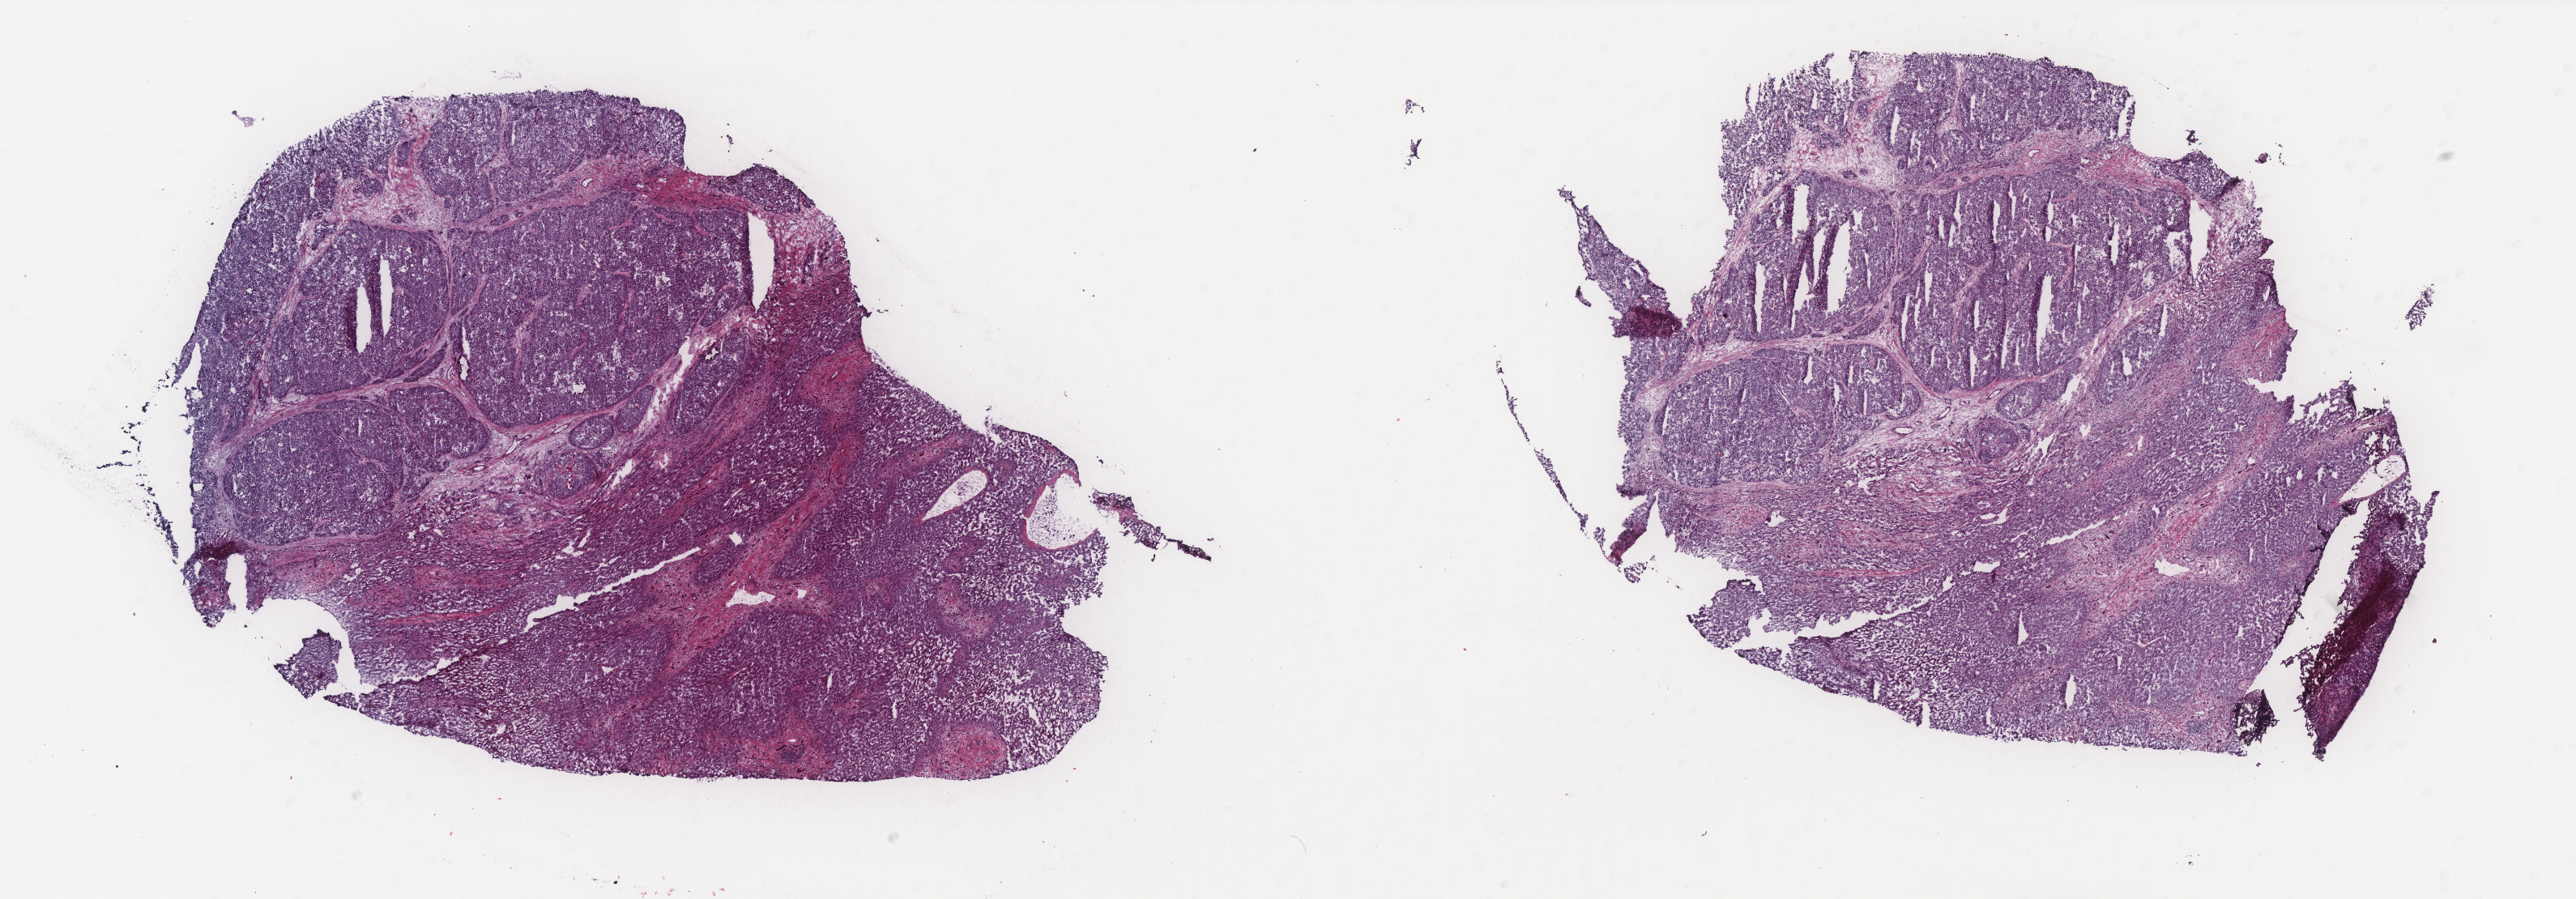
Digitized H&E tissue section (whole slide) — shown as a low-resolution overview of the whole scanned area (about 25.5 x 8.9 mm, slide scanned at 40x); frozen section; liver, primary tumour sample. Female patient; age at initial diagnosis 52 years. Histologic grade: G2 (moderately differentiated). Pathologist review of this section (percent, as recorded): tumour cells 50%, tumour nuclei 45%, normal cells 45%, stromal cells 5%, necrosis 0%. Inflammatory infiltration, as recorded: lymphocyte infiltration 0%, monocyte infiltration 0%, neutrophil infiltration 0%.
* AJCC pathologic stage: IIIA
* histologic diagnosis: Hepatocellular carcinoma, NOS